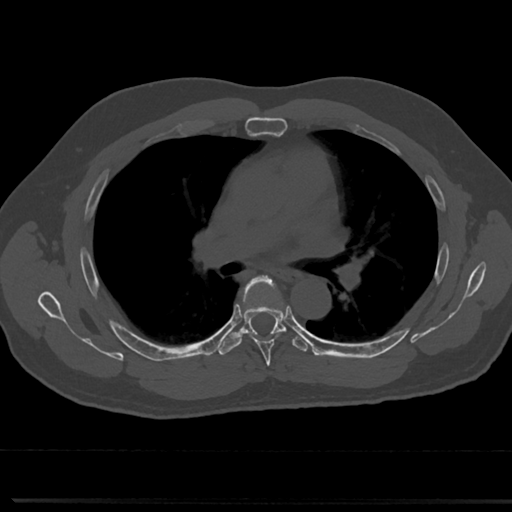
CT including the spine, one axial slice. Slice 475 of 817 in the series (ordered by position). Reconstruction kernel Br40s/3. Bone window (W 1800 / L 400 HU). 0.5 mm slice thickness. 512 × 512 image matrix, field of view 355 × 355 mm. Patient: male, 61 years. From the clinical record (not read from this slice): primary cancer: prostate.
Outlined on this slice (semi-automatic segmentation, software-assisted and operator-edited):
- T5 vertebra: bounding box (x1, y1, x2, y2) in pixels: (239, 277, 288, 360)
- T6 vertebra: (222, 323, 287, 350)